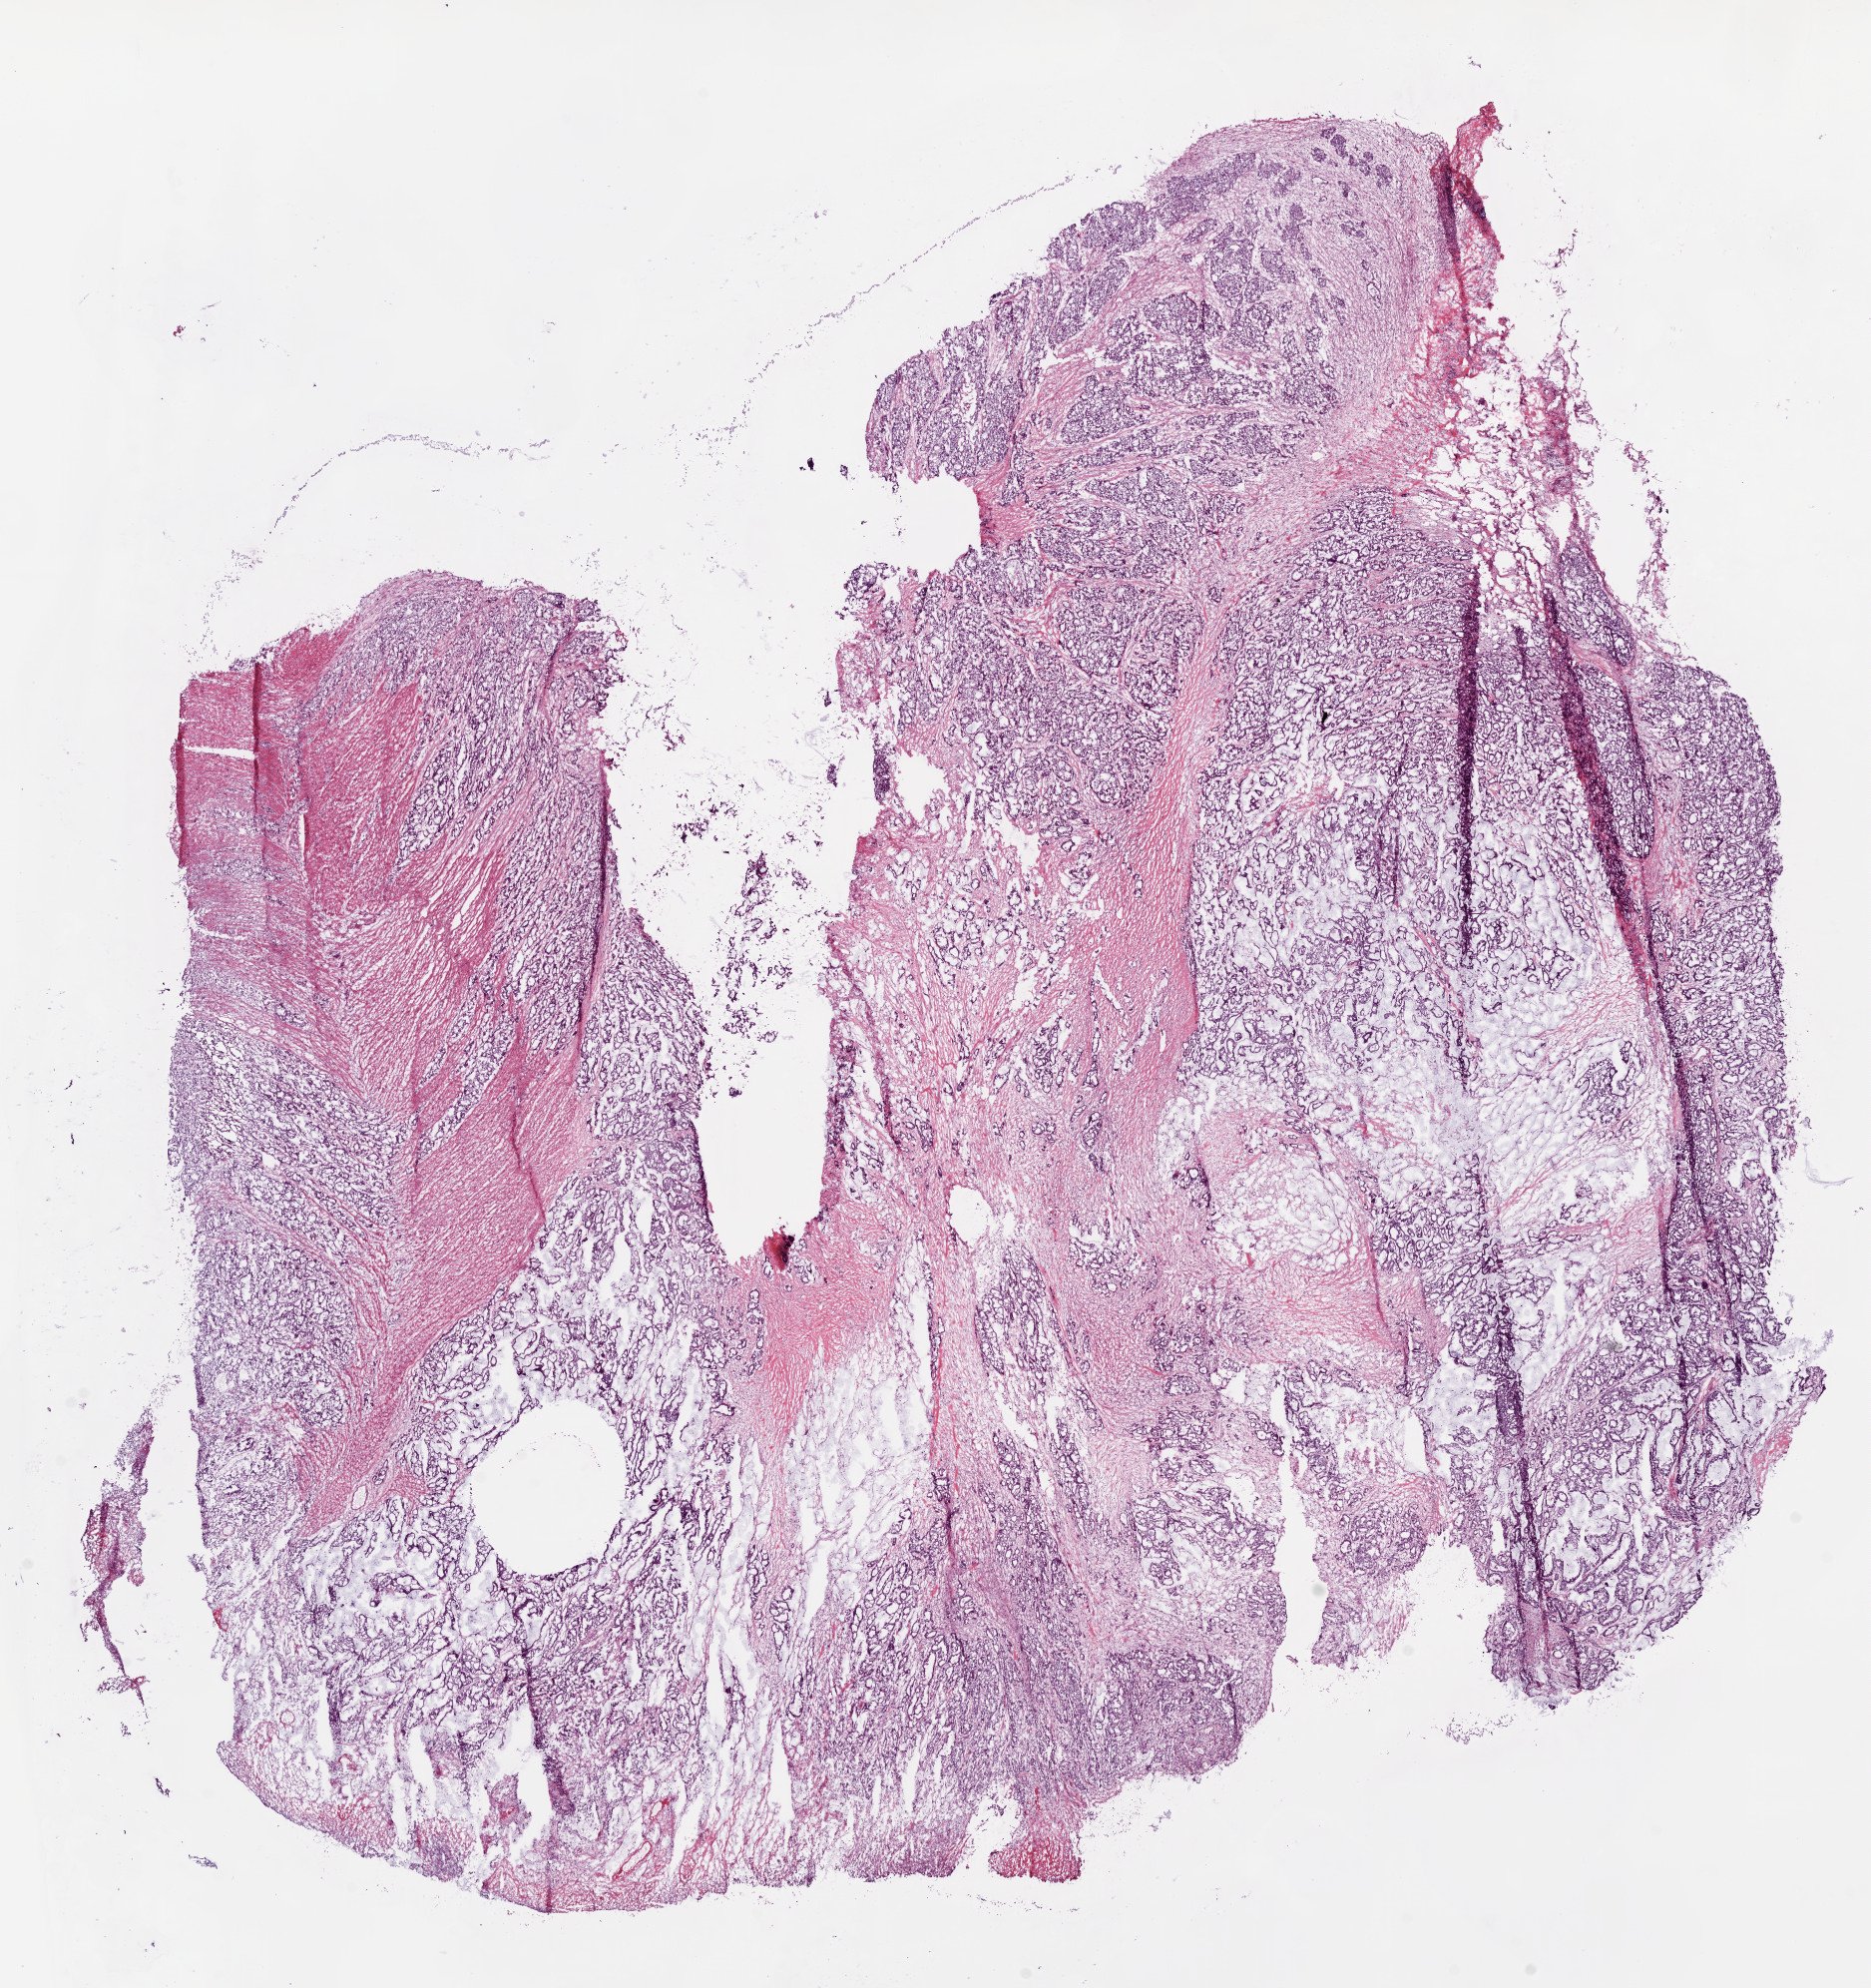
Whole-slide histology image, H&E — shown as a low-resolution overview of the whole scanned area (about 15.0 x 16.0 mm, acquisition: 20x scan), frozen section, primary tumour sample from the rectum. Male, age 51 years at initial diagnosis. Pathologist review of this section (percent, as recorded): tumour cells 65%, tumour nuclei 80%, normal cells 0%, stromal cells 30%, necrosis 5%.
* pathologic diagnosis: Mucinous adenocarcinoma
* AJCC pathologic stage: II (6th edition)